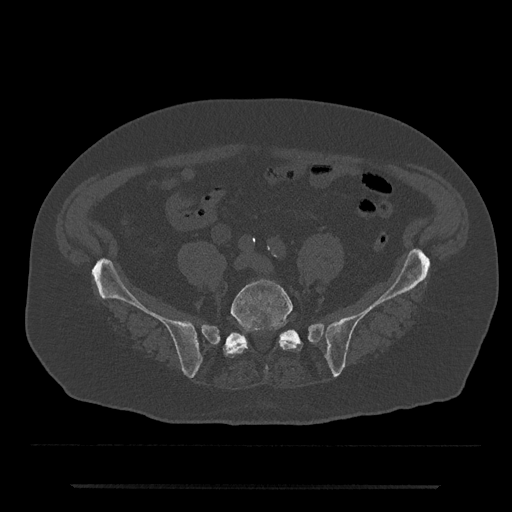
CT including the spine, one axial slice. Slice 270 of 797 in the series (ordered by position). Reconstruction kernel Br40s/3. Bone window (W 1800 / L 400 HU). 0.5 mm slice thickness. 512 × 512 image matrix, field of view 434 × 434 mm. Patient: male, 80 years. From the clinical record (not read from this slice): primary cancer: prostate; vertebrae with lytic lesions (as recorded): L1, T11.
Outlined on this slice (semi-automatic segmentation, software-assisted and operator-edited):
- L5 vertebra: bounding box <223,279,300,371> (left, top, right, bottom; pixels)